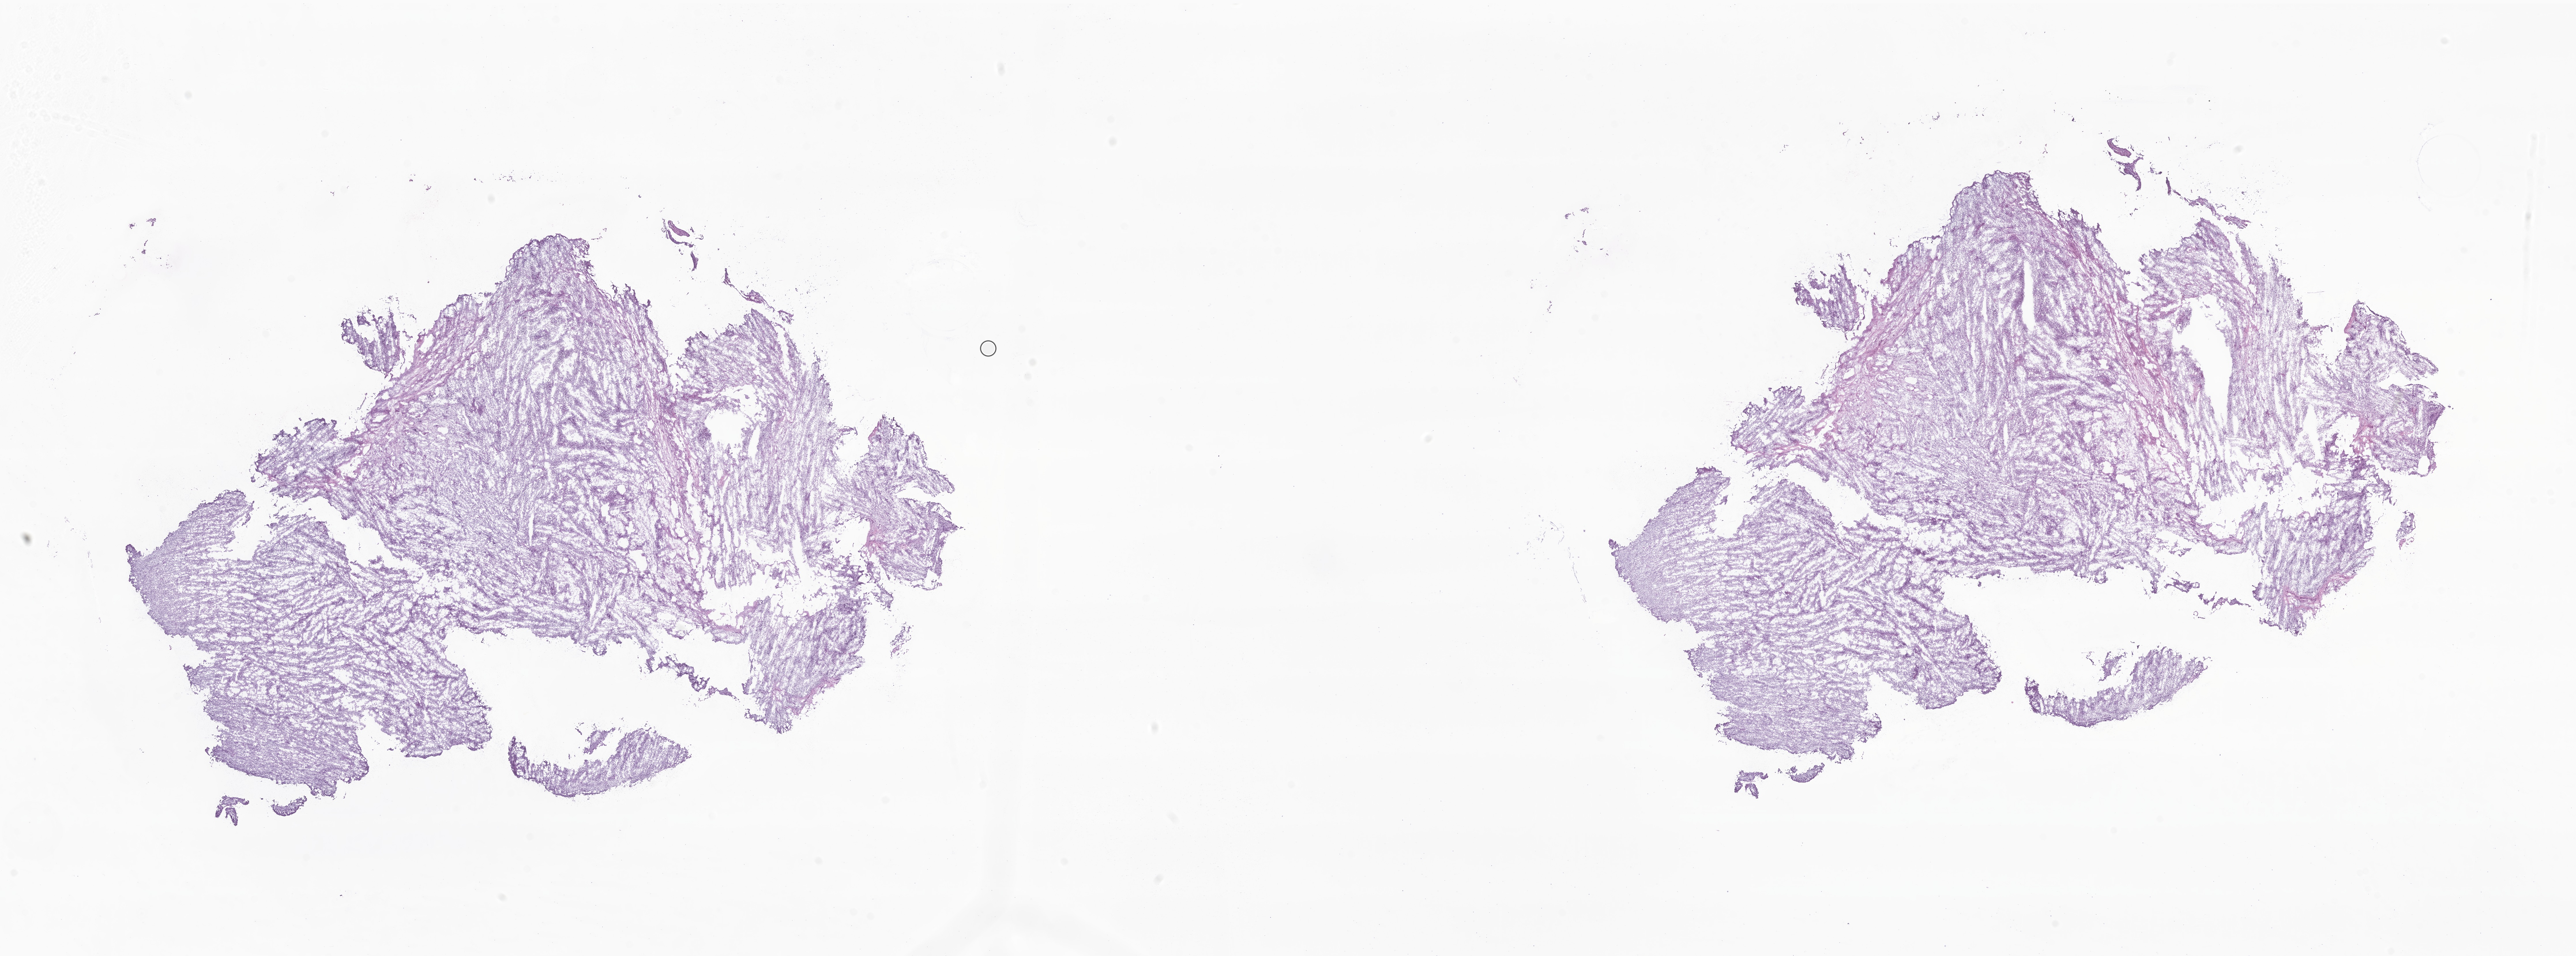
Digitized H&E-stained section of tumor tissue from the liver, low-resolution overview of the scanned area, about 37.7 x 14.0 mm; frozen section. Patient: male, age 46 months (3 years 10 months).
Diagnosis (ICD-O-3 morphology term): Spindle cell rhabdomyosarcoma.